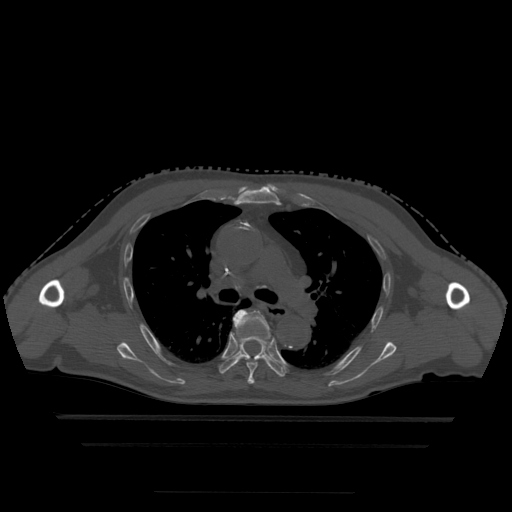
CT including the spine, one axial slice; position 327 of 522 along the scan axis; bone window (W 1800 / L 400 HU); 1.25 mm slice thickness; 512 × 512 image matrix, field of view 436 × 436 mm. Patient age 68 years. From the clinical record (not read from this slice): primary cancer: urothelial.
Outlined on this slice (semi-automatic segmentation, software-assisted and operator-edited):
- T5 vertebra: bounding box [x1, y1, x2, y2] px = [233, 310, 269, 384]
- T6 vertebra: [219, 331, 287, 378]